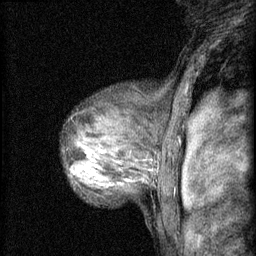
Breast MRI (dynamic contrast-enhanced), one sagittal slice; slice 47 of 60 in the series (ordered by position); 3 images stored at this slice position (order not interpretable as contrast timing); 1.5 T; TE 4.2 ms, TR 8.2 ms; 256 × 256 image matrix, field of view 180 × 180 mm. Female patient, age 48 years.
Annotated regions visible in this slice (semi-automatic segmentation, software-assisted and operator-edited):
- analysis volume of interest (the breast-tissue region the enhancement analysis was run in; not a lesion): bounding box (x1, y1, x2, y2) in pixels: (70, 138, 133, 191)
- tumour enhancement mask (voxels above the 70 % enhancement threshold inside the analysis volume of interest): (72, 150, 127, 181)